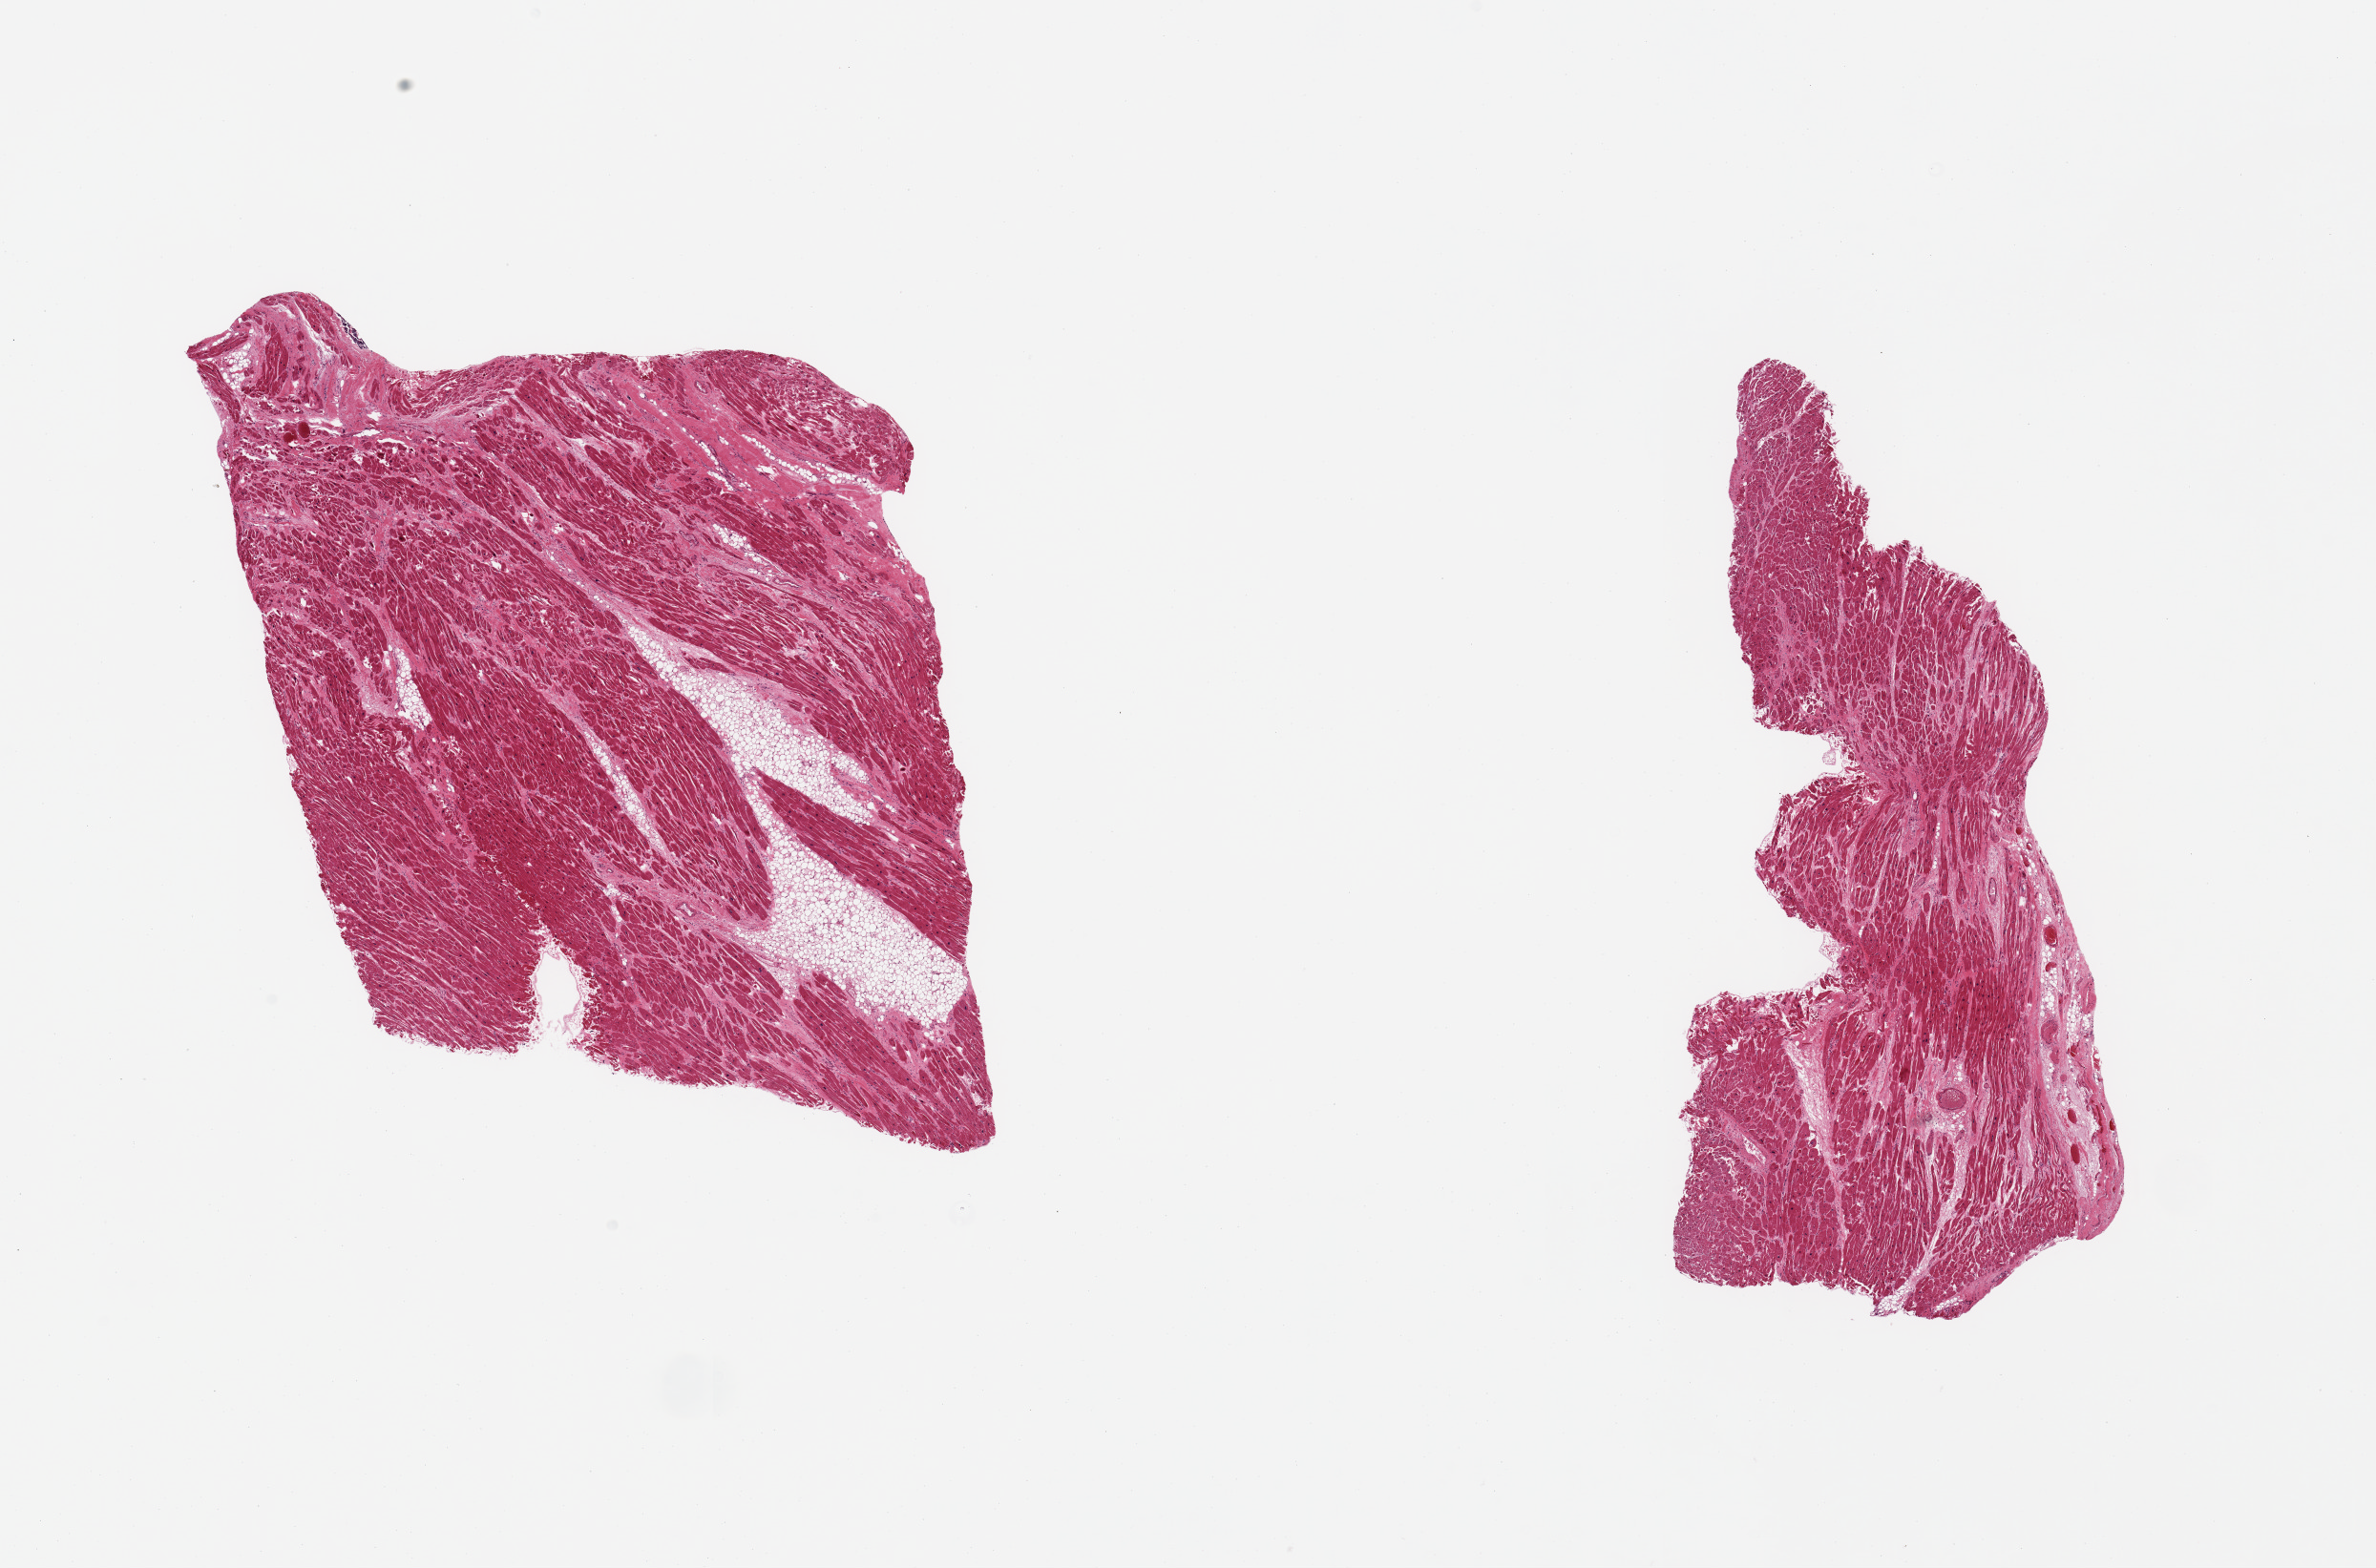
Haematoxylin and eosin whole-slide image, whole scanned area (about 19.7 x 13.0 mm, acquisition: 20x scan) shown as a low-resolution overview, PAXgene-fixed, paraffin-embedded tissue, section of heart (target tissue), tissue donor sample. Male donor.
Pathologist's review note for this sample: 2 pieces; moderate patchy fibrosis & 10% internal fat; no inflammation.